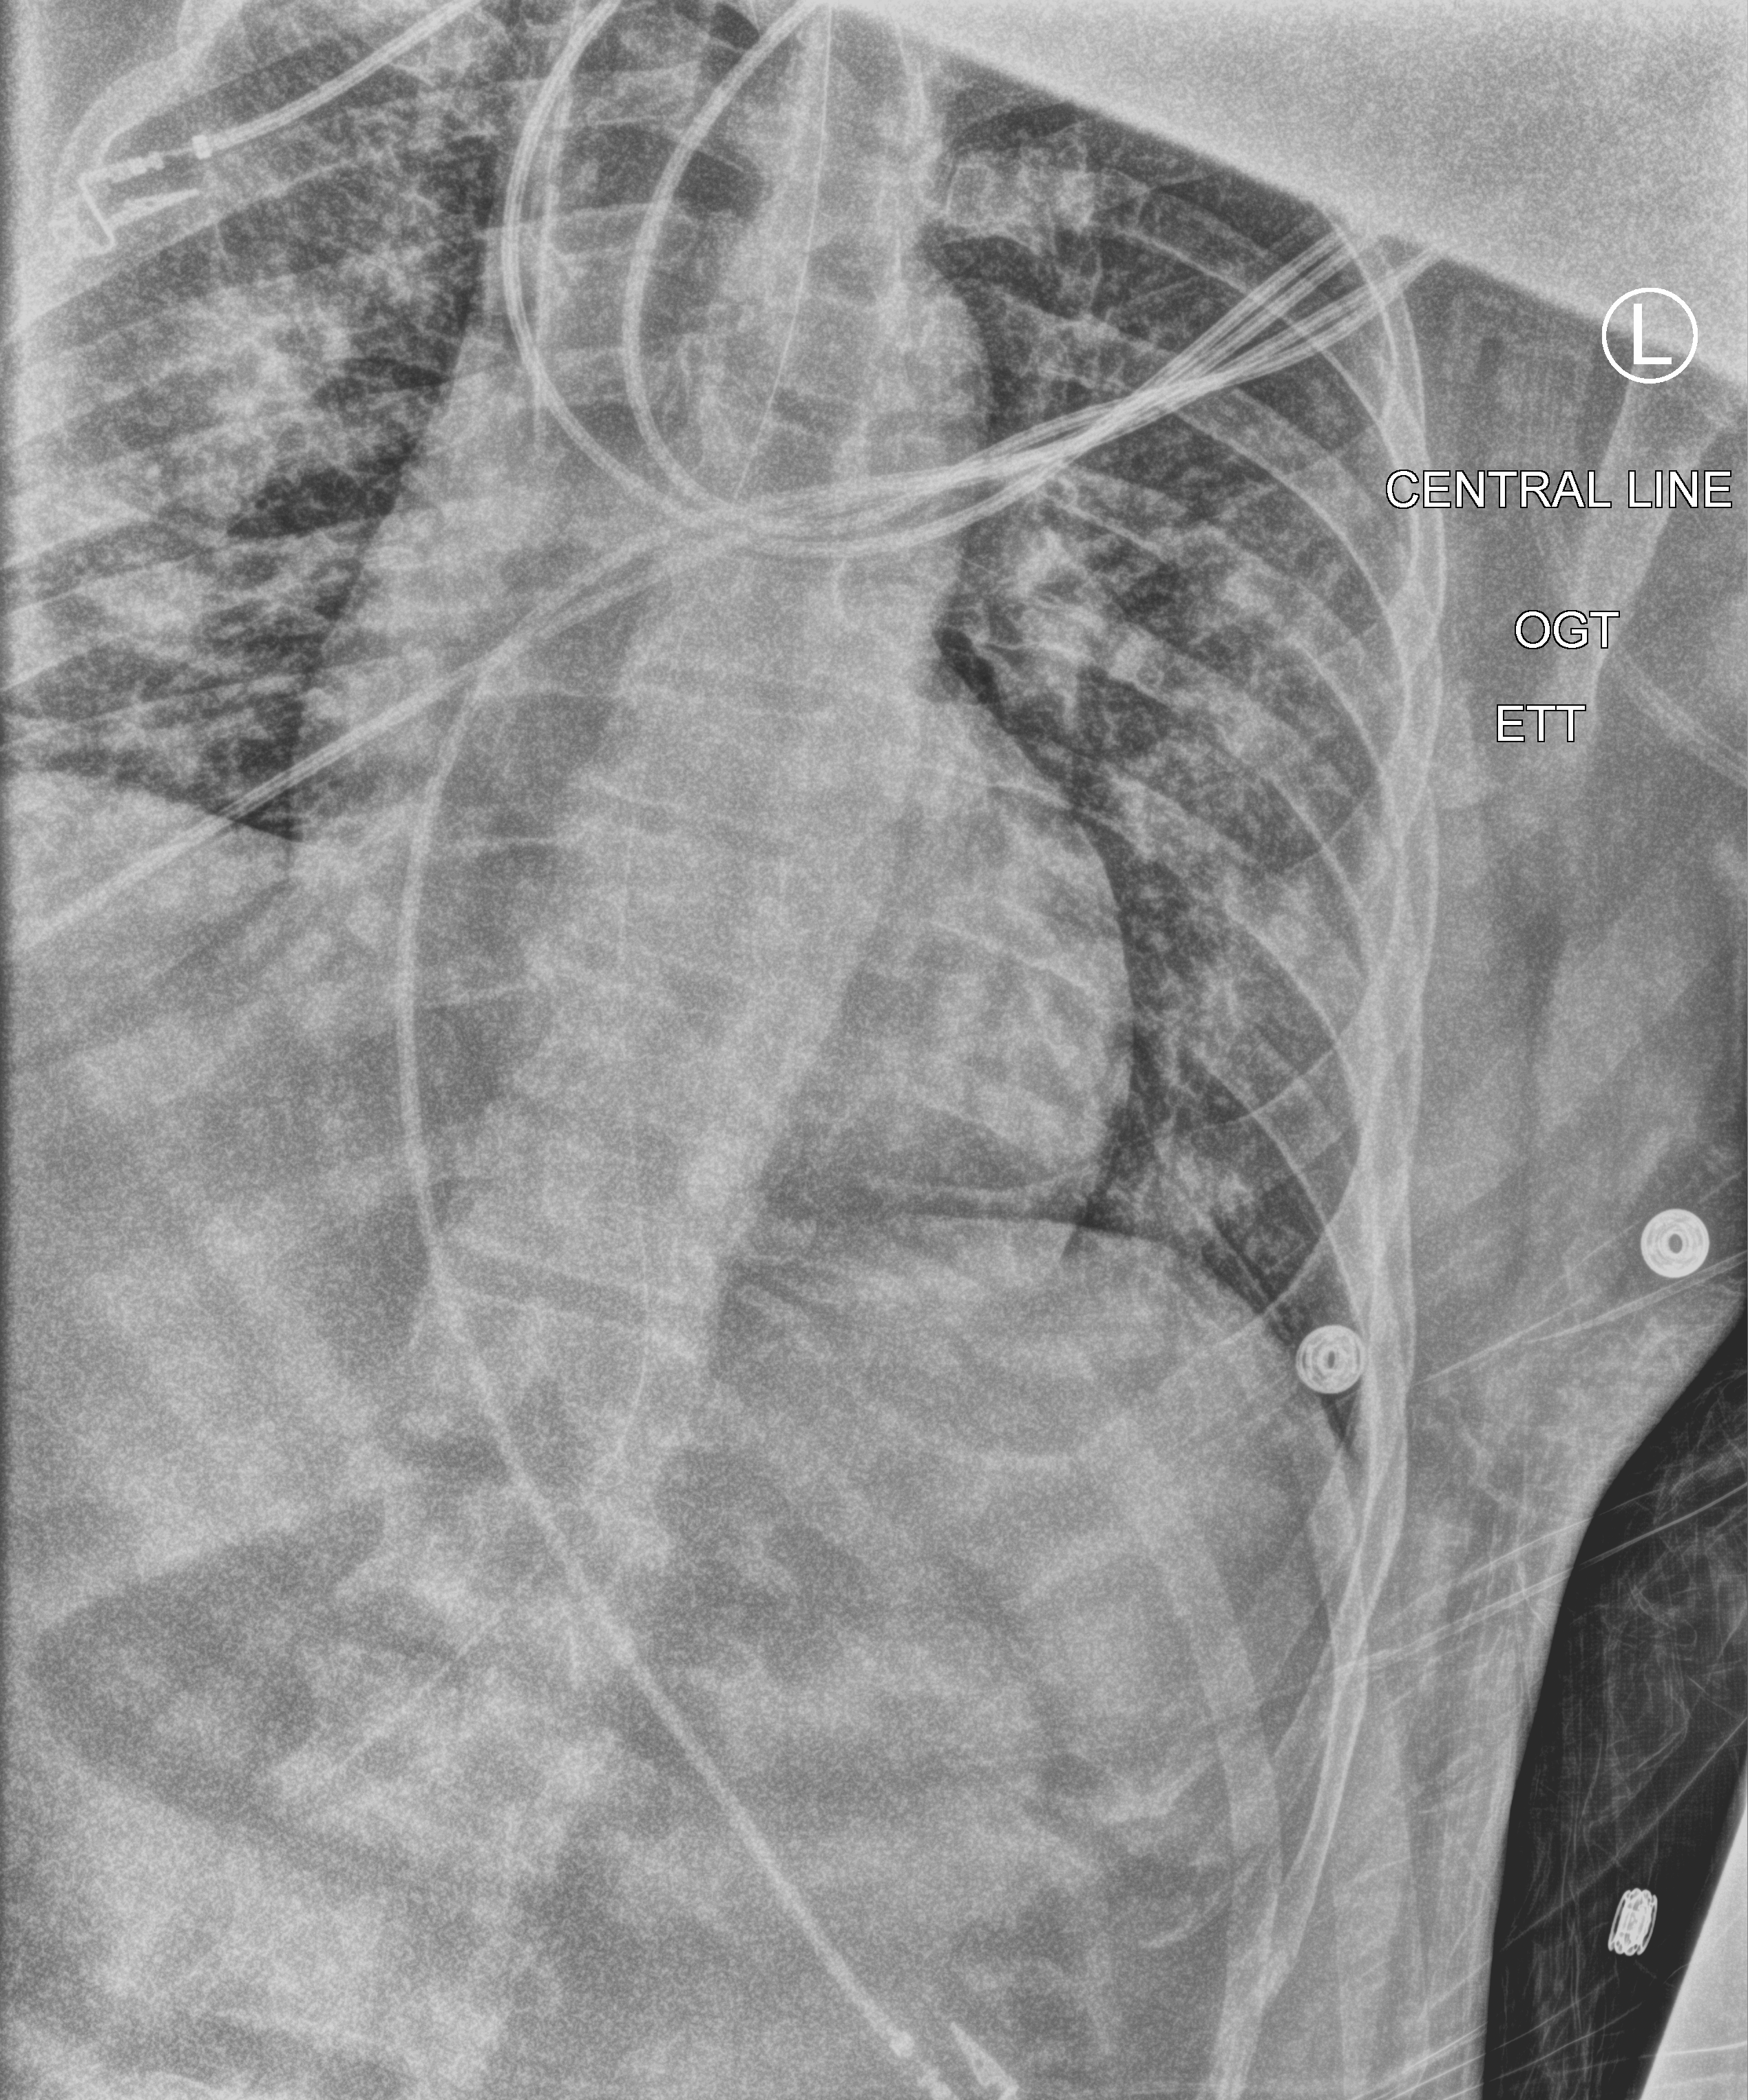
Portable chest radiograph, anteroposterior (AP) projection. Patient hospitalised with COVID-19; male, aged 18–59 years.
Admission-level facts for this patient (not findings on this image; timing relative to this image not recorded): mechanically ventilated during this hospital stay: yes; admitted to intensive care during this hospital stay: no.